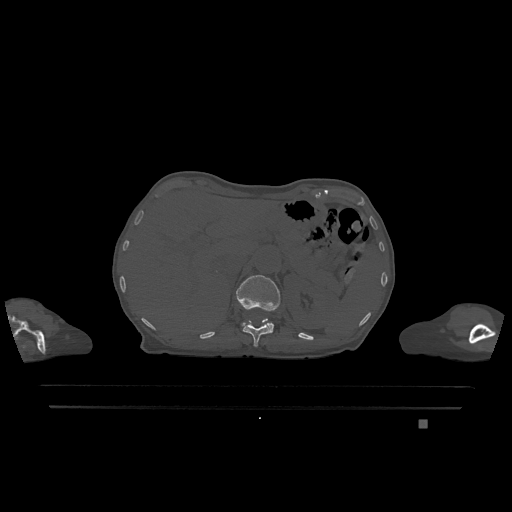
CT including the spine, one axial slice. Slice 508 of 1317 in the series (ordered by position). Bone window (W 1800 / L 400 HU). 0.5 mm slice thickness. 512 × 512 image matrix, field of view 500 × 500 mm. Female patient, age 74 years. Case-level facts recorded for this patient, not image findings: primary cancer: lung; vertebrae with lytic lesions (as recorded): T1, T4, T5, T6, L4, L5.
Outlined on this slice (semi-automatic segmentation, software-assisted and operator-edited):
- L1 vertebra: box from (x=236, y=275) to (x=280, y=332) px
- T12 vertebra: (x=243, y=319)–(x=272, y=347)